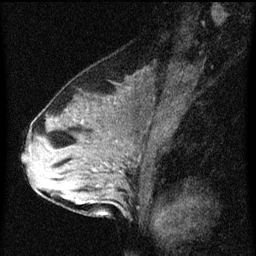
Breast MRI (dynamic contrast-enhanced), one sagittal slice. Slice 30 of 60 in the series (ordered by position). Dynamic contrast-enhanced series, image 2 of 3 at this slice position (ordered by acquisition). 1.5 T. TE 4.2 ms, TR 8 ms. 2 mm slice thickness. 256 × 256 image matrix, field of view 180 × 180 mm. Female patient, age 33 years.
Structures marked on this image (semi-automatic segmentation, software-assisted and operator-edited):
- analysis volume of interest (the breast-tissue region the enhancement analysis was run in; not a lesion): bounding box <61,126,142,213> (left, top, right, bottom; pixels)
- tumour enhancement mask (voxels above the 70 % enhancement threshold inside the analysis volume of interest): <81,168,96,205>